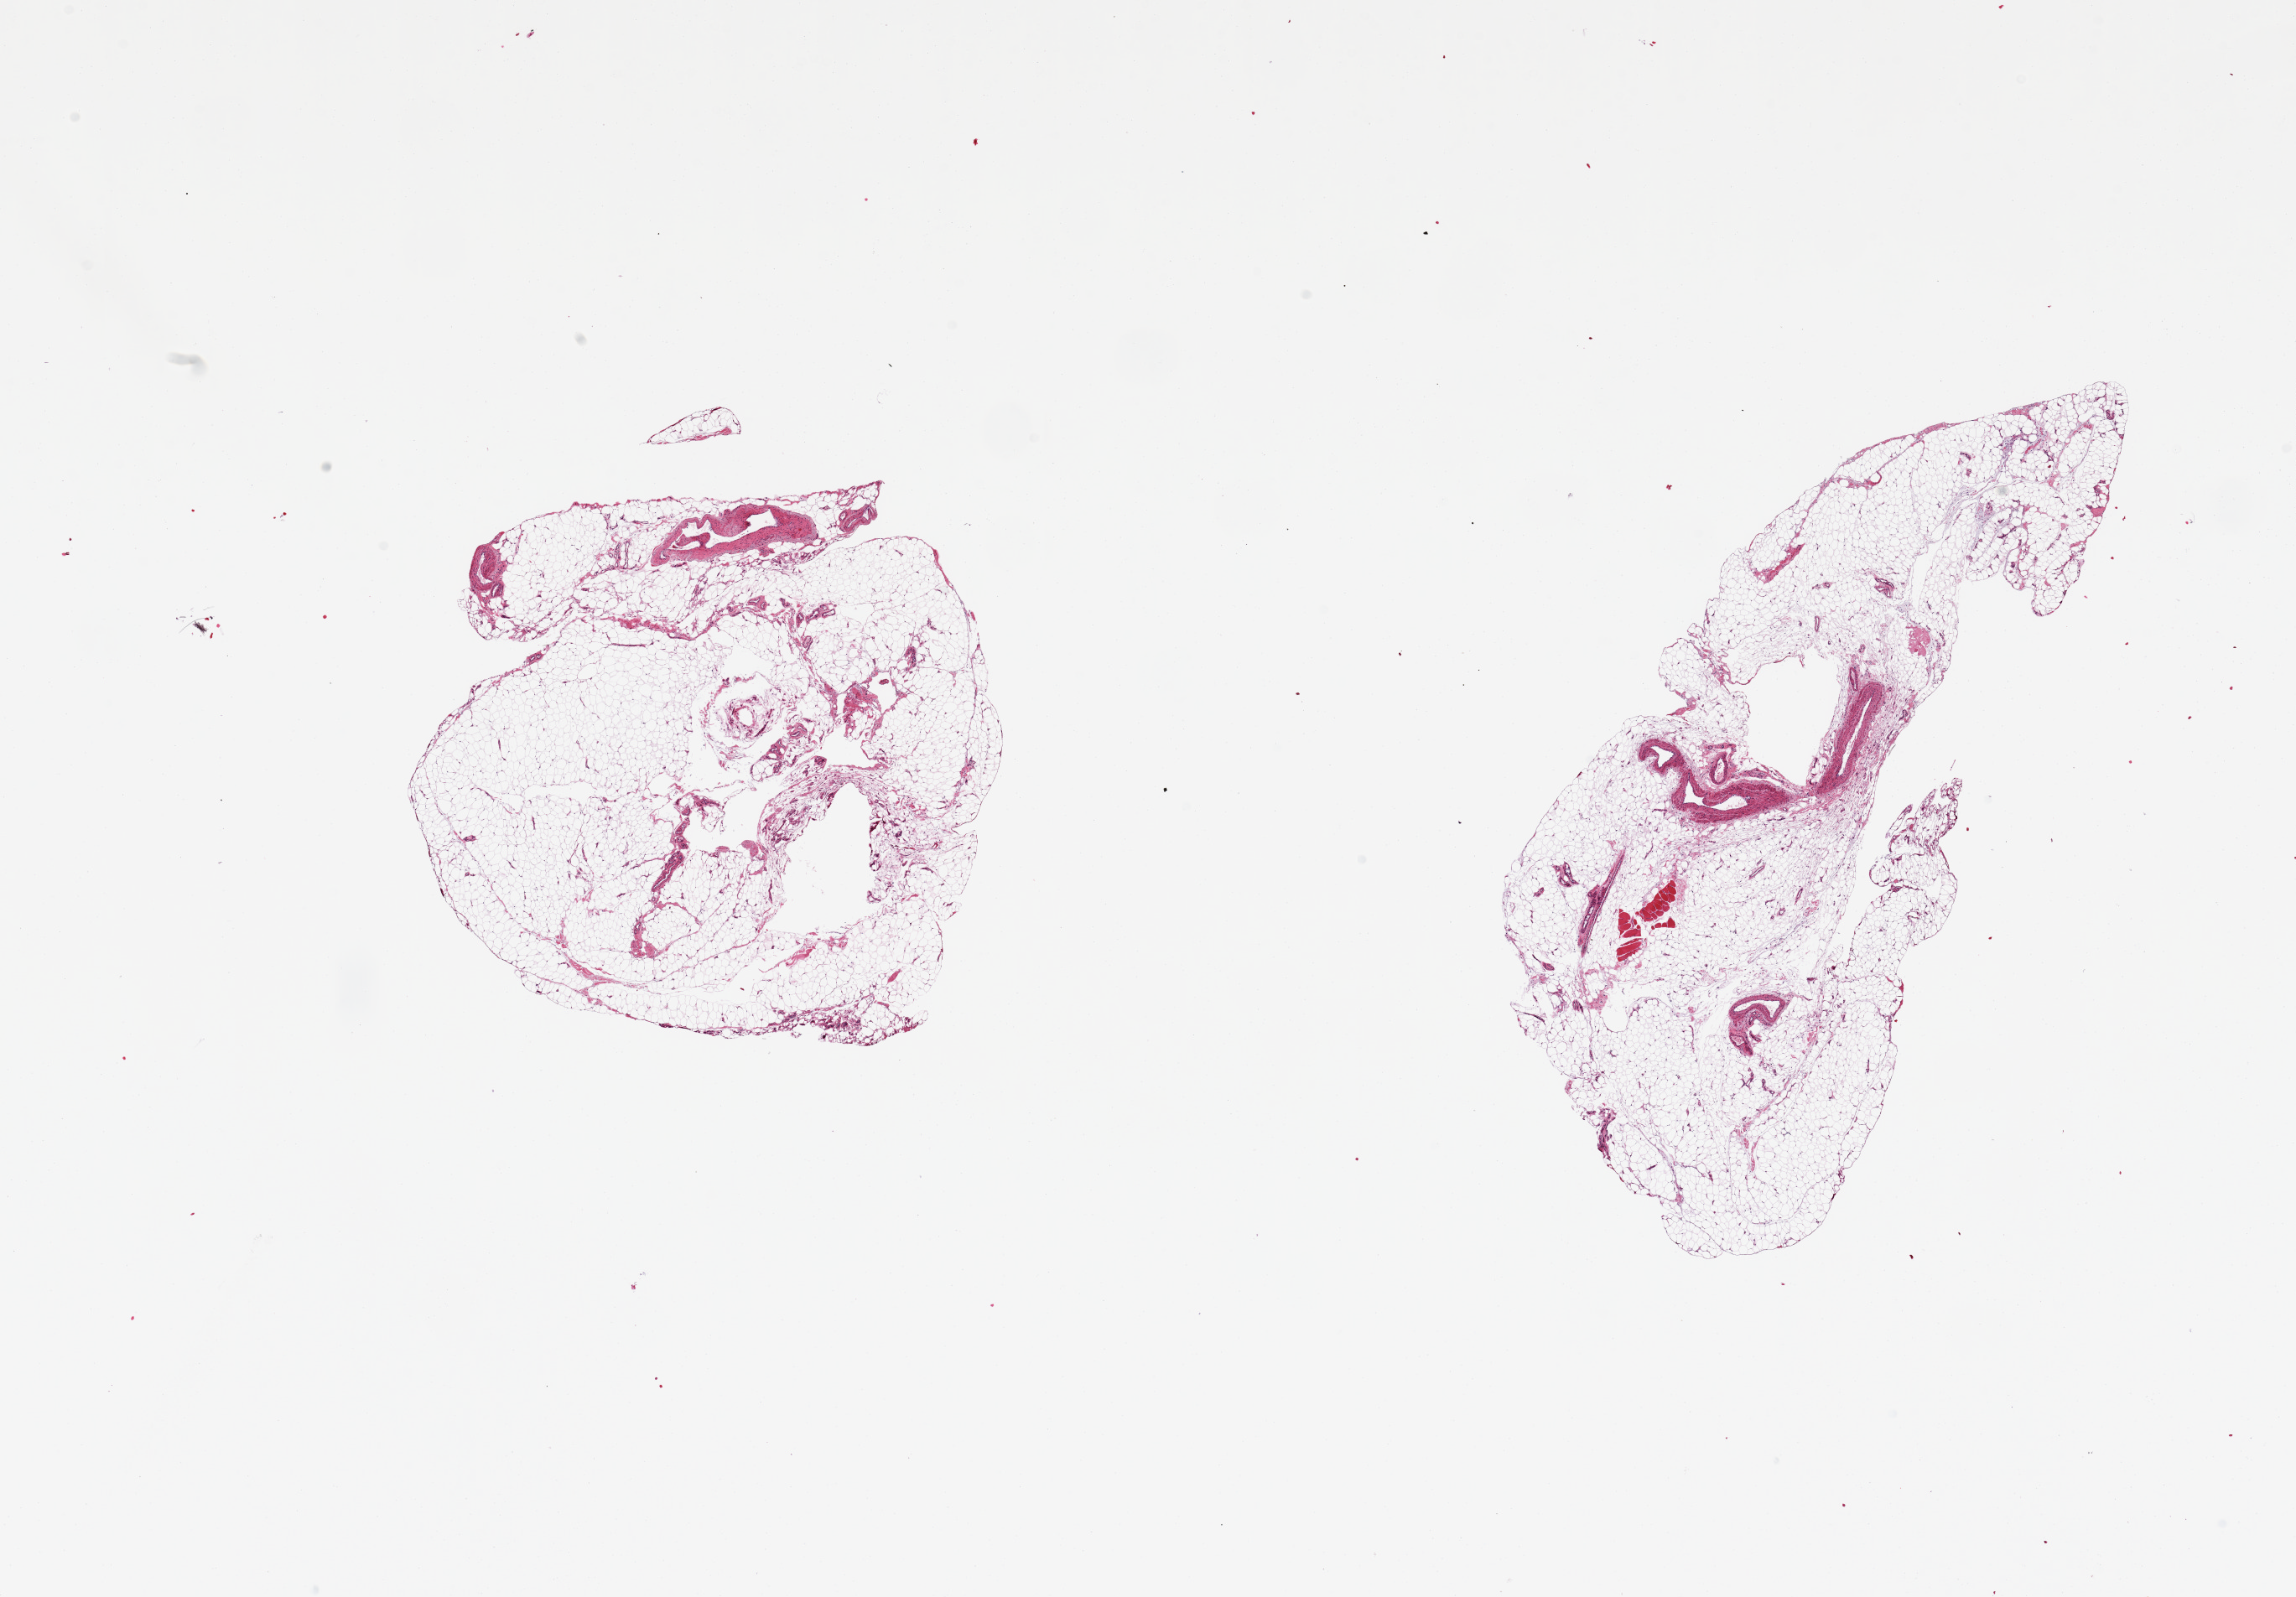
Whole-slide image, hematoxylin and eosin (H&E) stain, a low-resolution overview of the entire scanned area, about 21.7 x 15.1 mm; PAXgene-fixed paraffin-embedded (PFPE) section; sampled site (target tissue): adipose tissue; tissue donor sample. Donor sex: male.
Pathologist's review note for this sample: 2 pieces; 5% vascular content.